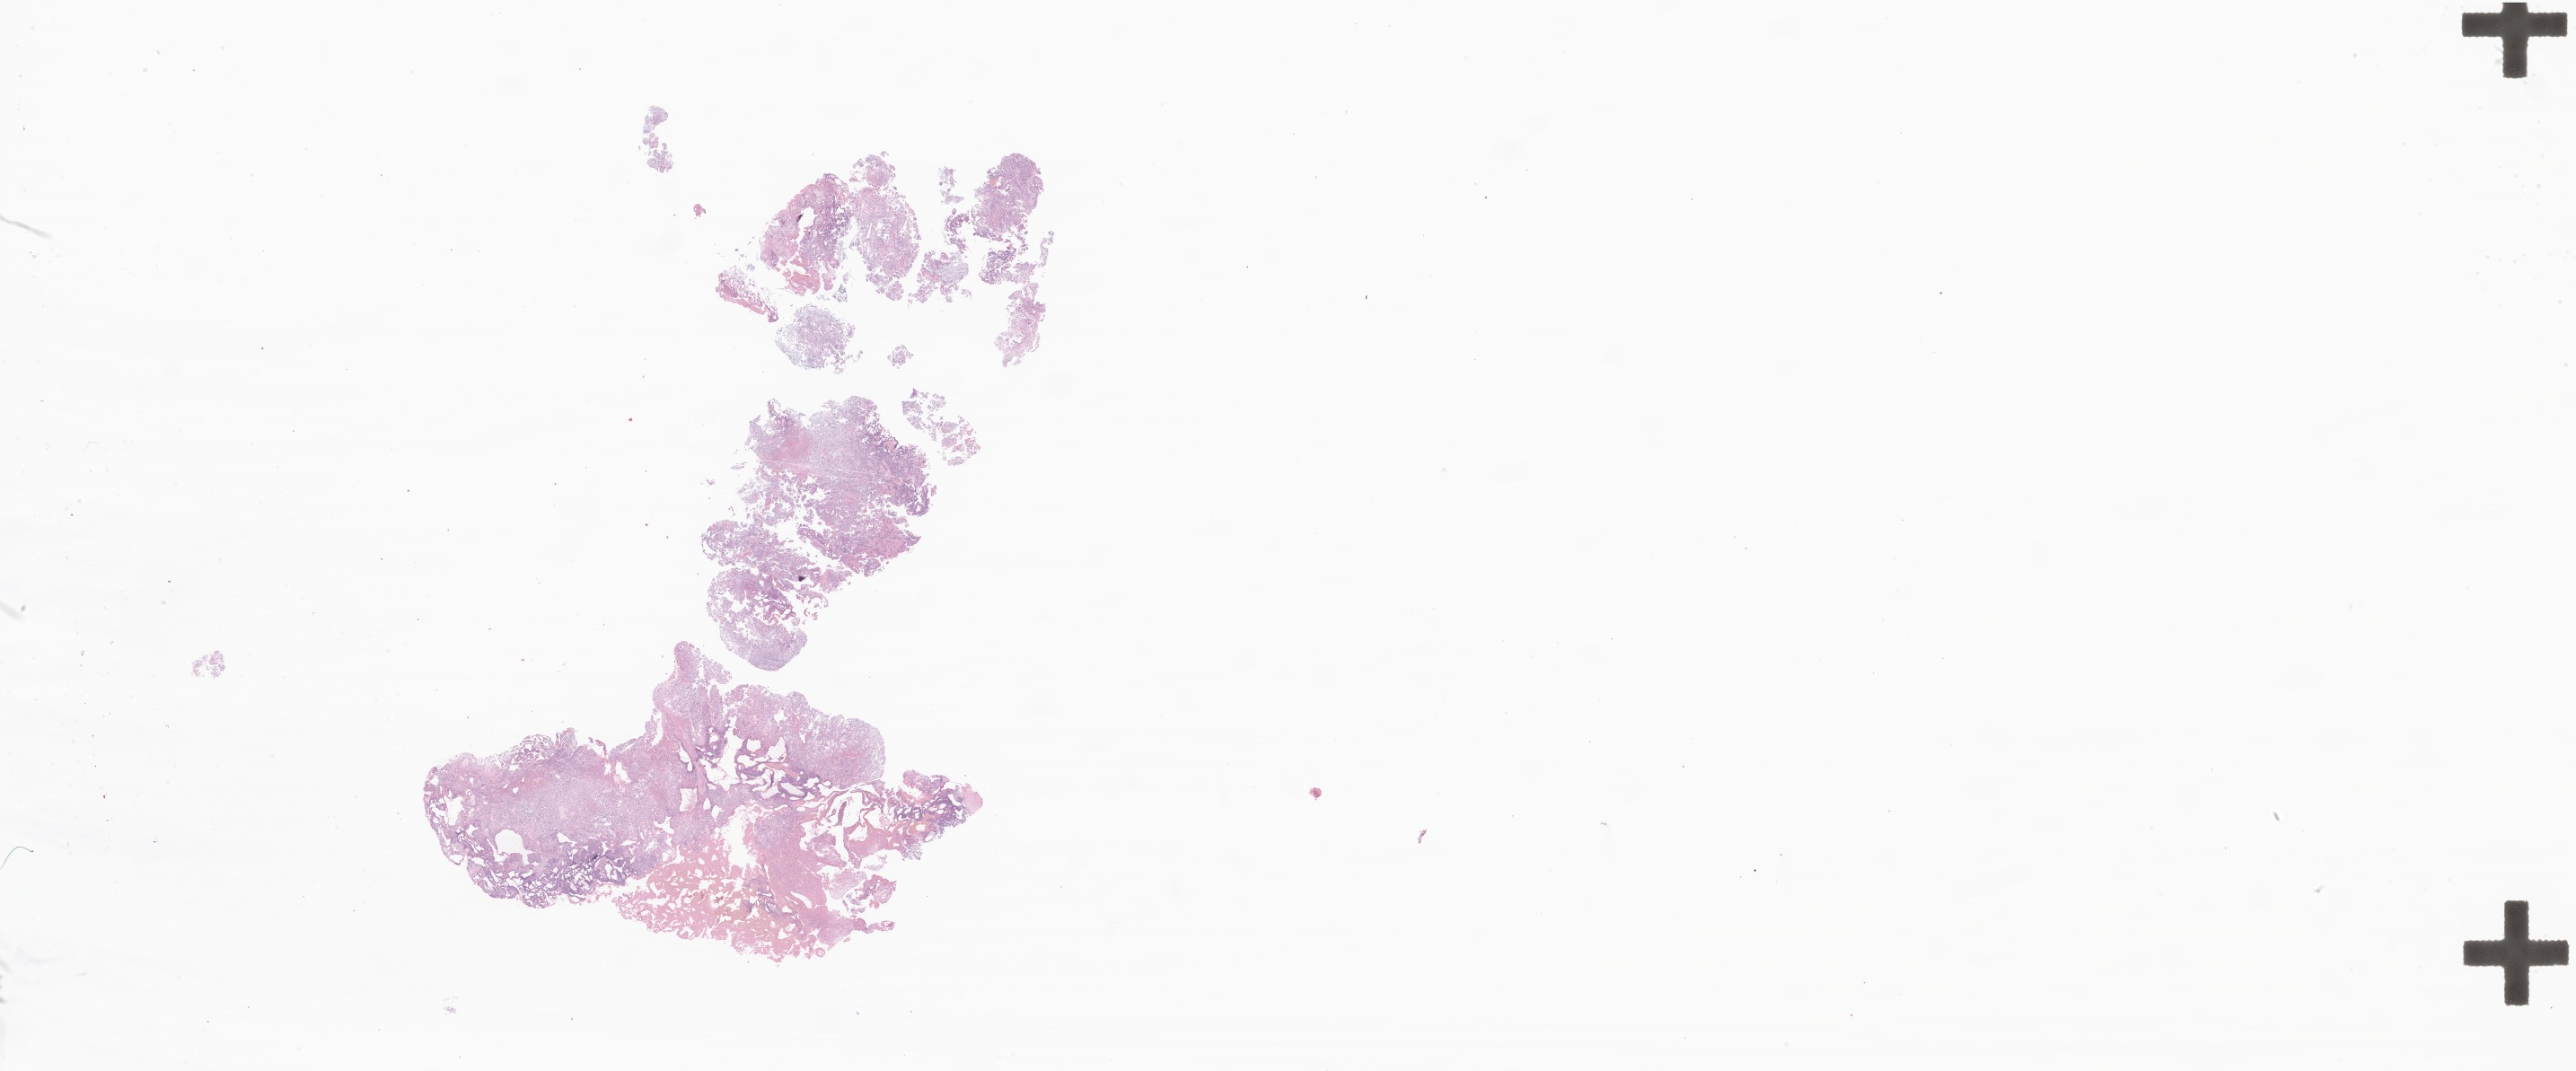
Digitized hematoxylin and eosin (H&E)-stained section of tumor tissue from the brain — a low-resolution overview of the entire scanned area, about 48.4 x 20.1 mm. FFPE section. Male patient, age 97 months.
Recorded diagnosis: Pinealoma.